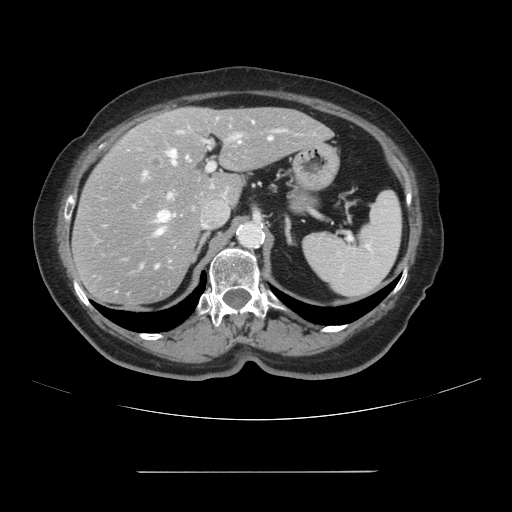
Contrast-enhanced abdominal CT, one axial slice; position 66 of 111 along the scan axis; 120 kVp; intravenous contrast given; soft-tissue window (W 400 / L 40 HU); 2.5 mm slice thickness; 512 × 512 image matrix, field of view 400 × 400 mm. Female patient, age 74 years. From the clinical record (not read from this slice): diagnosis: colorectal cancer liver metastases, imaged before liver resection; multiple liver metastases: yes; largest metastasis: 1.1 cm; chemotherapy before resection: yes.
Structures marked on this image (manually delineated by an expert):
- hepatic veins: bounding box (x1, y1, x2, y2) in pixels: (157, 137, 273, 234)
- liver: (74, 108, 331, 307)
- planned liver remnant (the part of the liver to remain after resection): (149, 108, 330, 205)
- portal vein (with intrahepatic branches): (141, 117, 317, 200)
- liver metastasis: (151, 157, 160, 166)